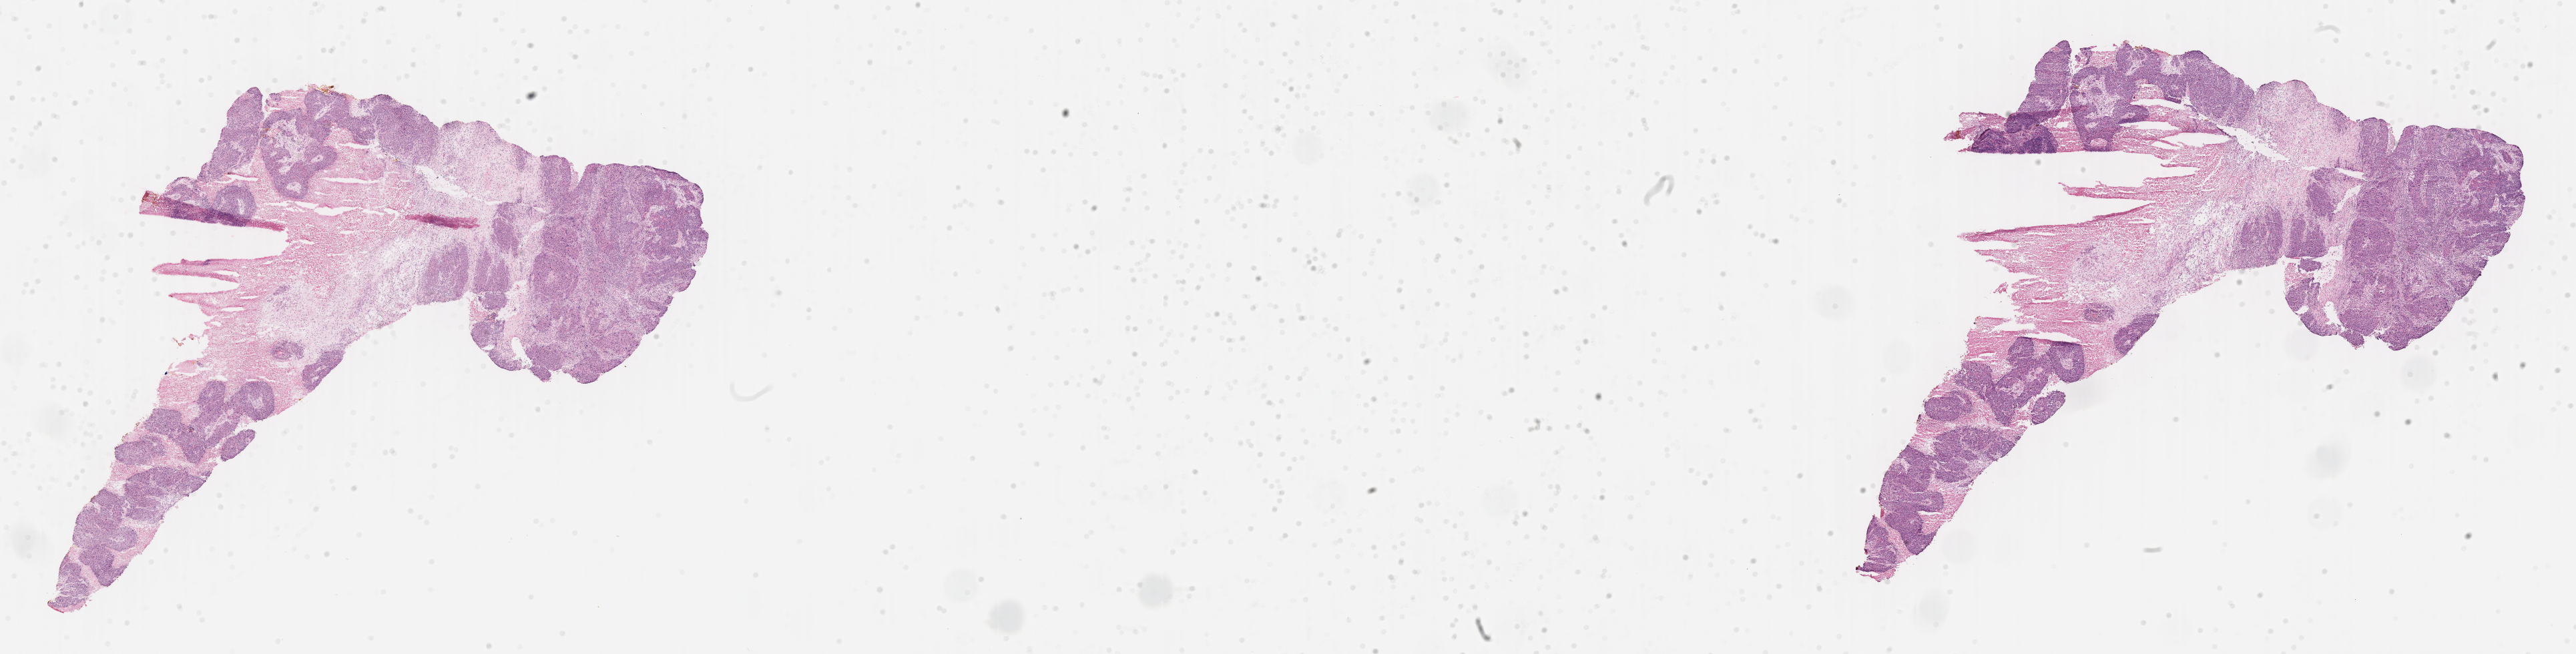
Hematoxylin and eosin (H&E) whole-slide image — whole scanned area (about 31.1 x 7.9 mm) shown as a low-resolution overview; frozen section (tissue freezing medium); primary tumor; site: breast (right). Patient: female, age at initial diagnosis 41 years. Composition of this section per pathologist review: tumor cells 75%, tumor nuclei 75%, stromal cells 15%, necrosis 10%, normal cells 0%. Infiltration values recorded for this section: lymphocyte infiltration 4%, monocyte infiltration 2%, neutrophil infiltration 5%.
- histologic diagnosis: Infiltrating duct carcinoma, NOS
- section: top of the tissue portion